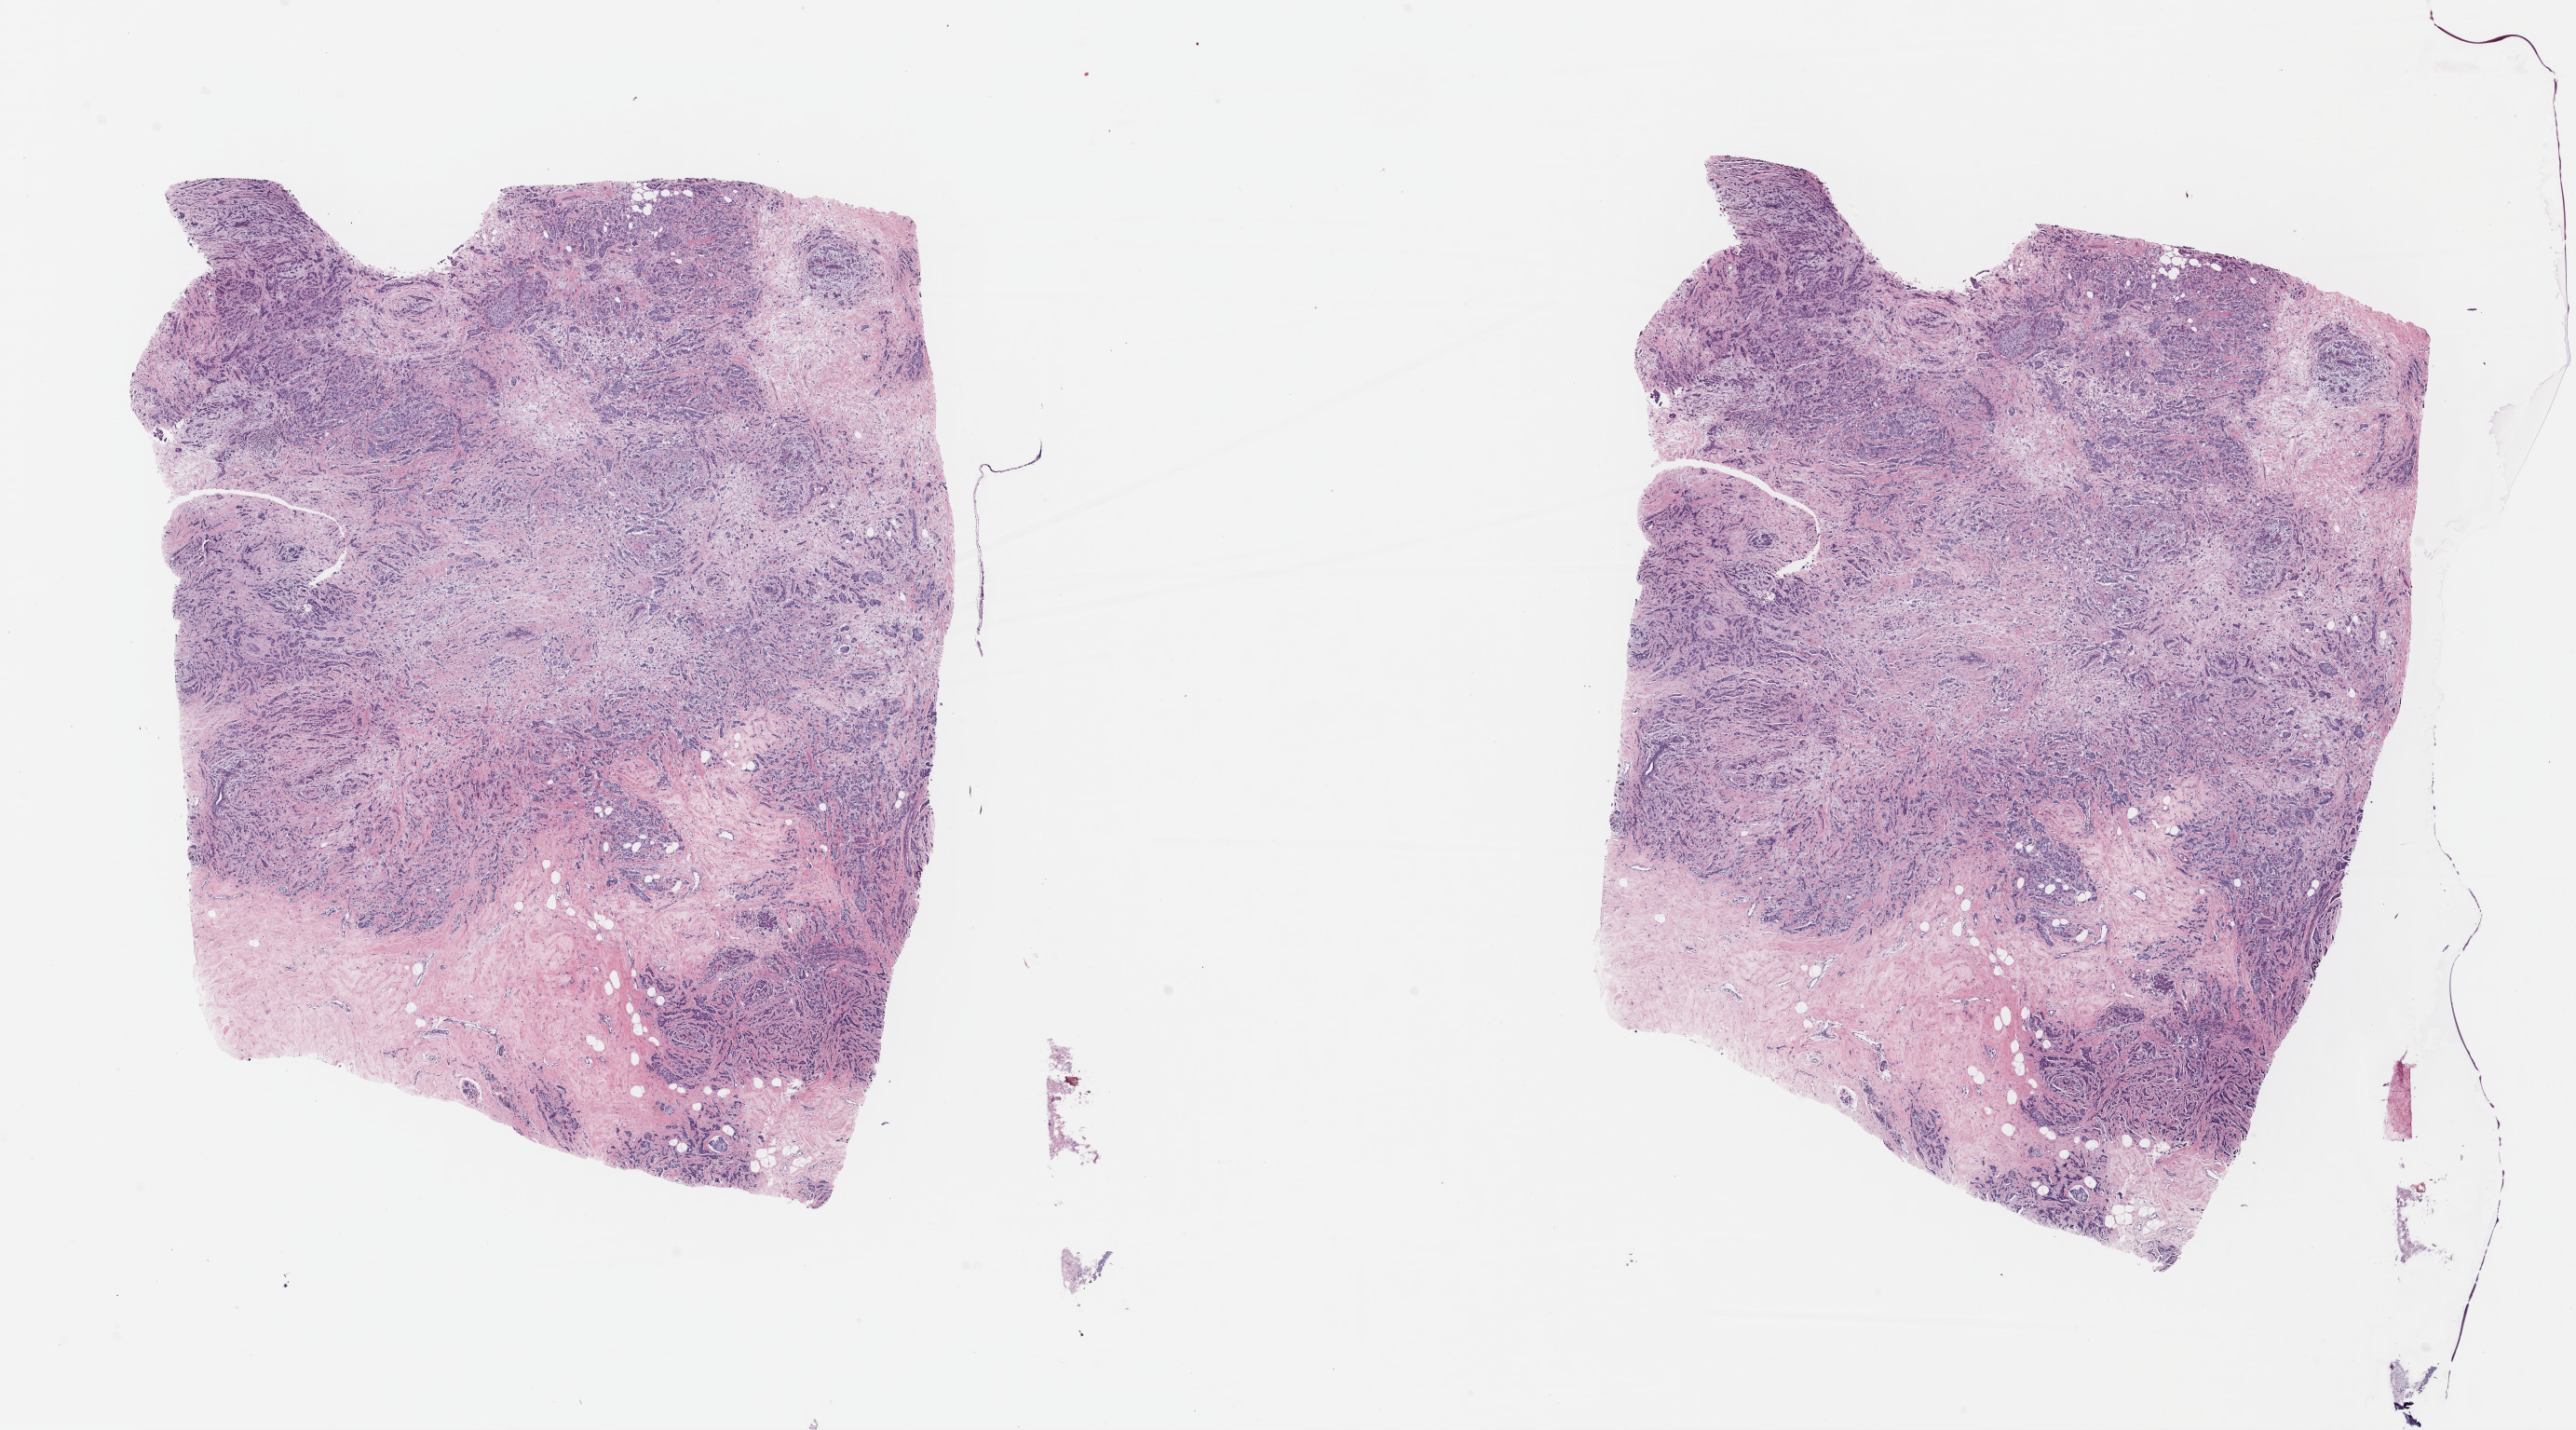
Whole-slide histology image, H&E-stained — shown as a low-resolution overview of the whole scanned area (about 21.7 x 12.1 mm, acquisition: 40x scan). Formalin-fixed paraffin-embedded (FFPE) diagnostic section. Breast, primary tumour sample. Female patient; age at initial diagnosis 44 years.
- TNM: T3 N1a M0
- AJCC pathologic stage: IIIA
- lymph nodes positive (case pathology): 3 of 11 examined
- histologic diagnosis: Infiltrating duct carcinoma, NOS
- laterality: right